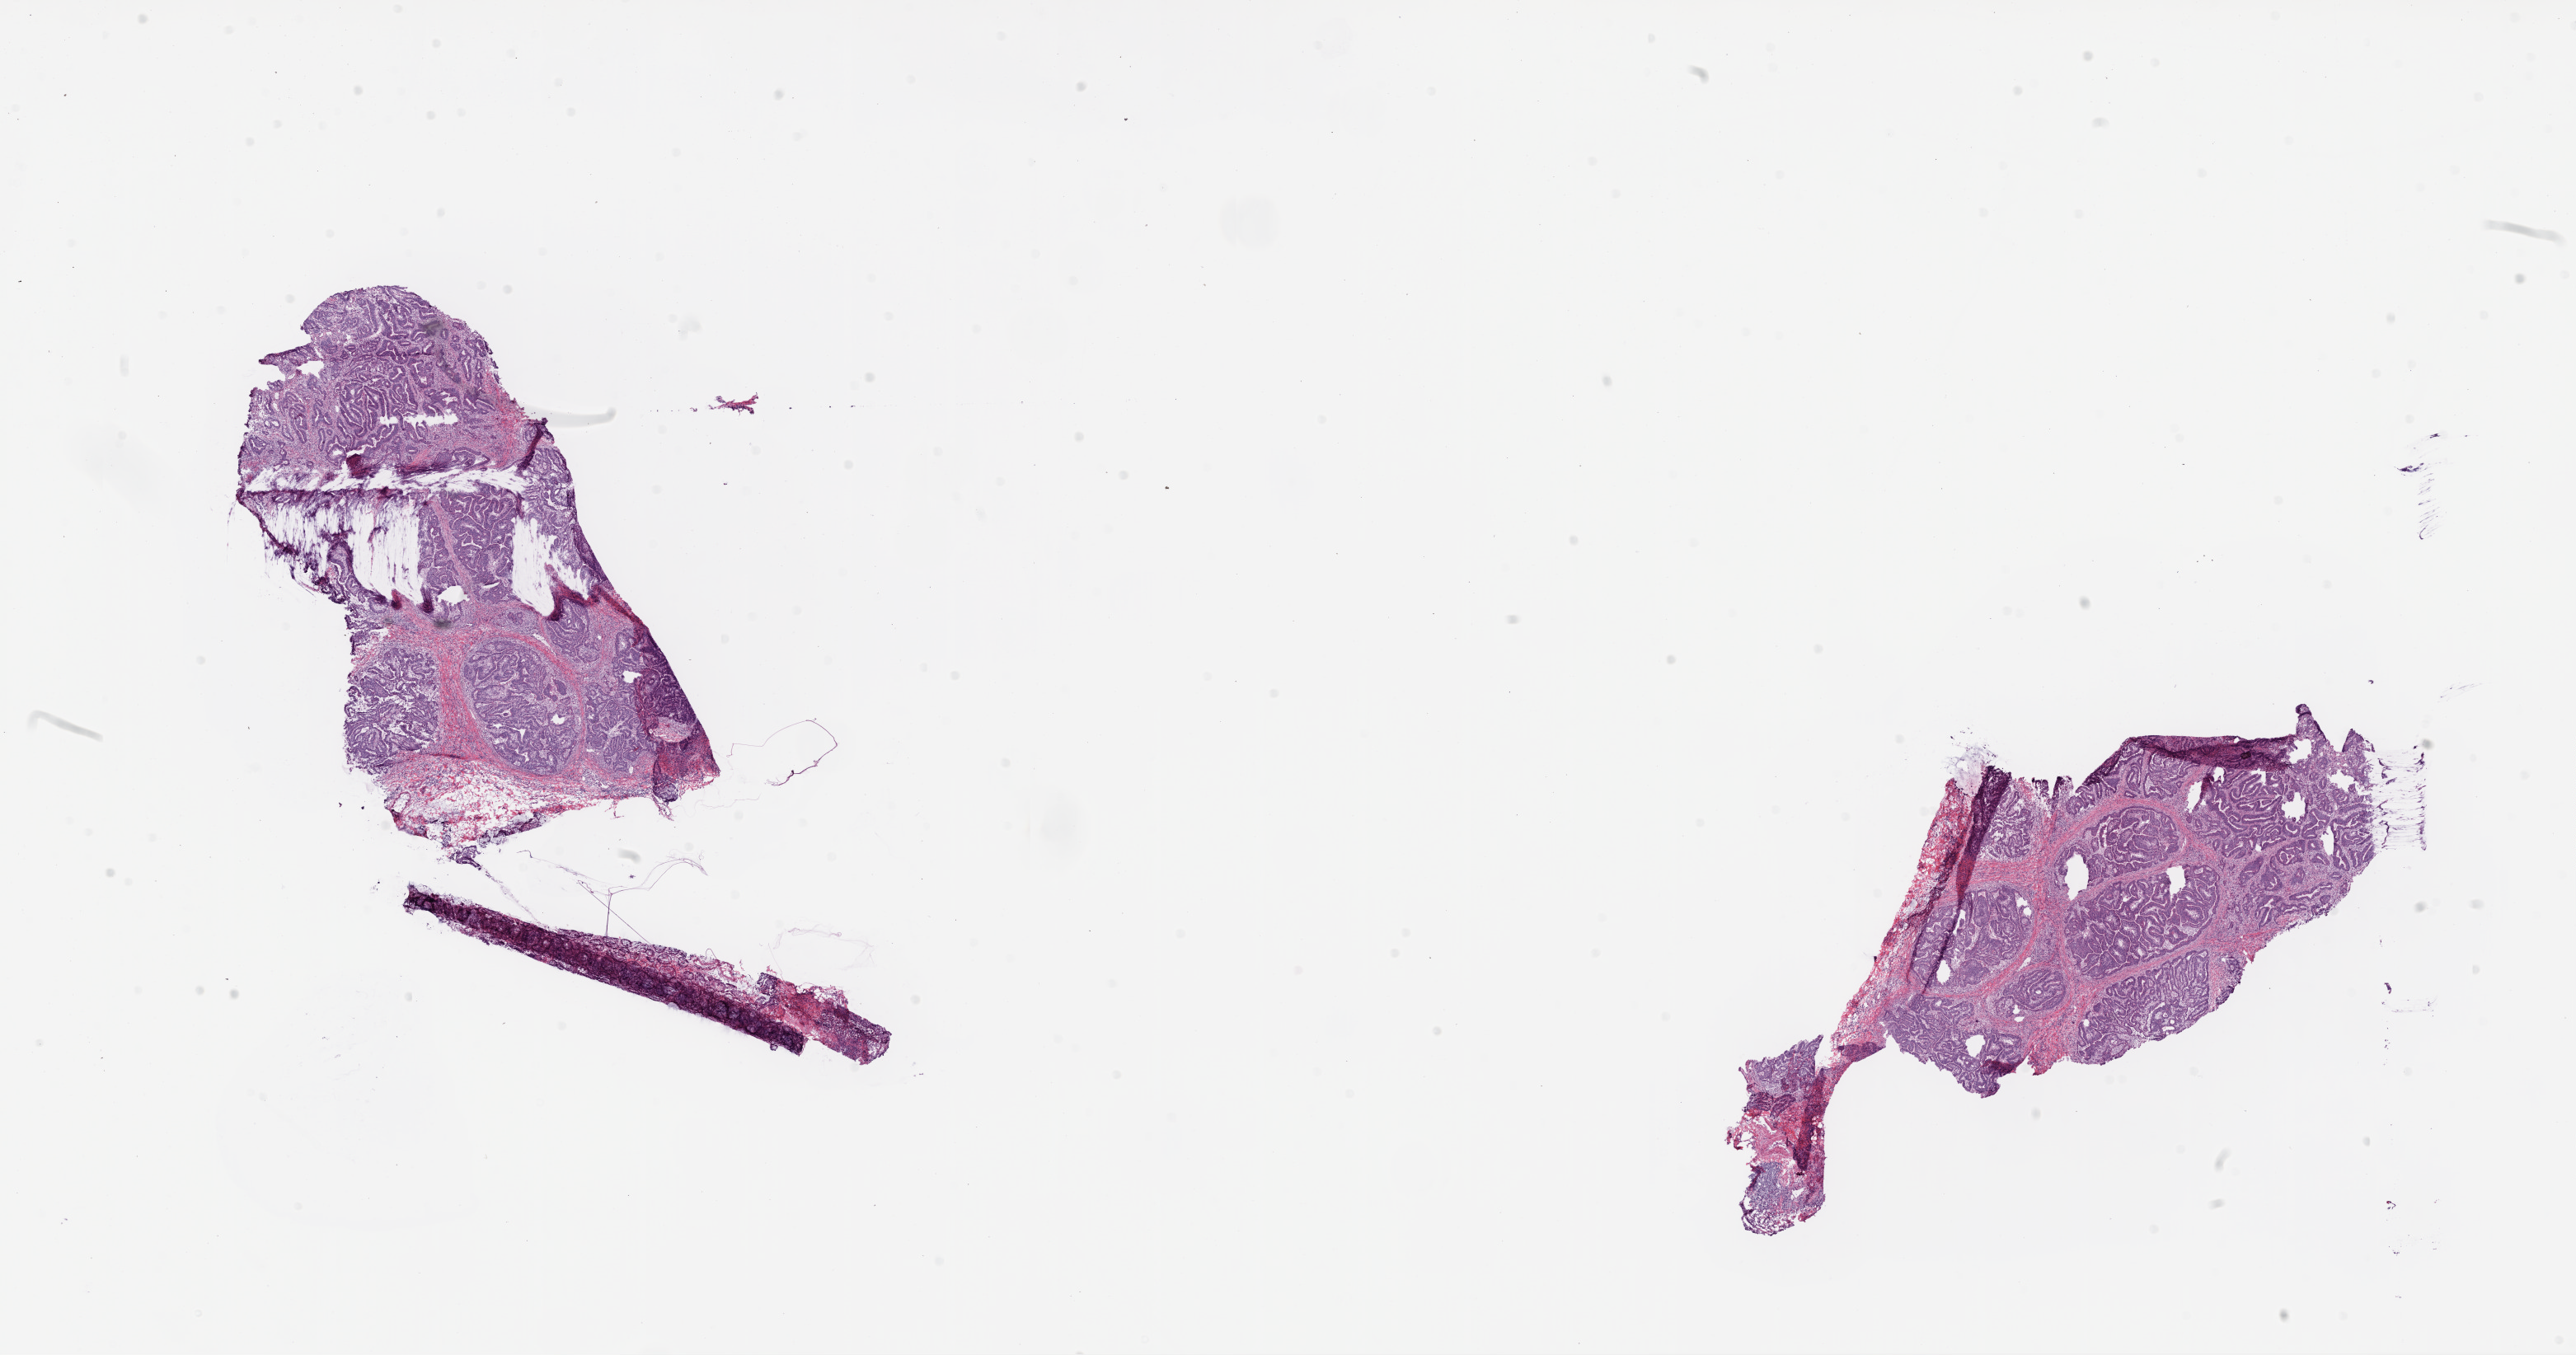
H&E whole-slide image, shown as a low-resolution overview of the whole scanned area (about 25.1 x 13.2 mm, from a 20x scan). Frozen section. Colon, primary tumour sample. Male patient; age at initial diagnosis 68 years. Pathologist review of this section (percent, as recorded): tumour cells 65%, tumour nuclei 85%, normal cells 0%, stromal cells 35%, necrosis 0%.
TNM: T2 N0 M0. AJCC pathologic stage: I. Lymph nodes positive (case pathology): 0 of 21 examined. Pathologic diagnosis: Adenocarcinoma, NOS.